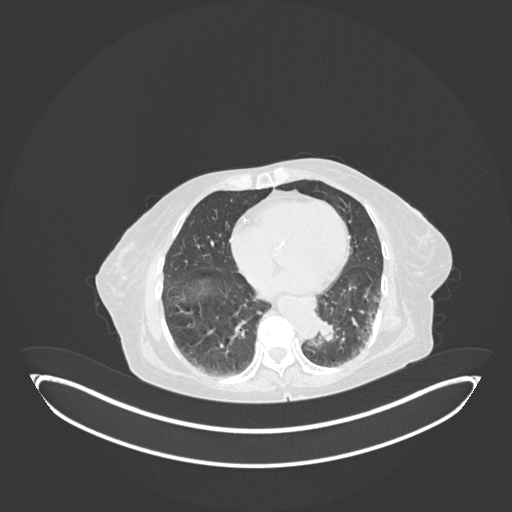
Chest CT, one axial slice; lung window (W 1500 / L -600 HU); 512 × 512 image matrix. Patient: female, 82 years. Case-level facts recorded for this patient, not image findings: clinical TNM (as recorded): T1b N0 M1.
Structures marked on this image (bounding box drawn by a radiologist):
- lung tumour (recorded histology: adenocarcinoma): bounding box (x1, y1, x2, y2) in pixels: (314, 314, 340, 348)